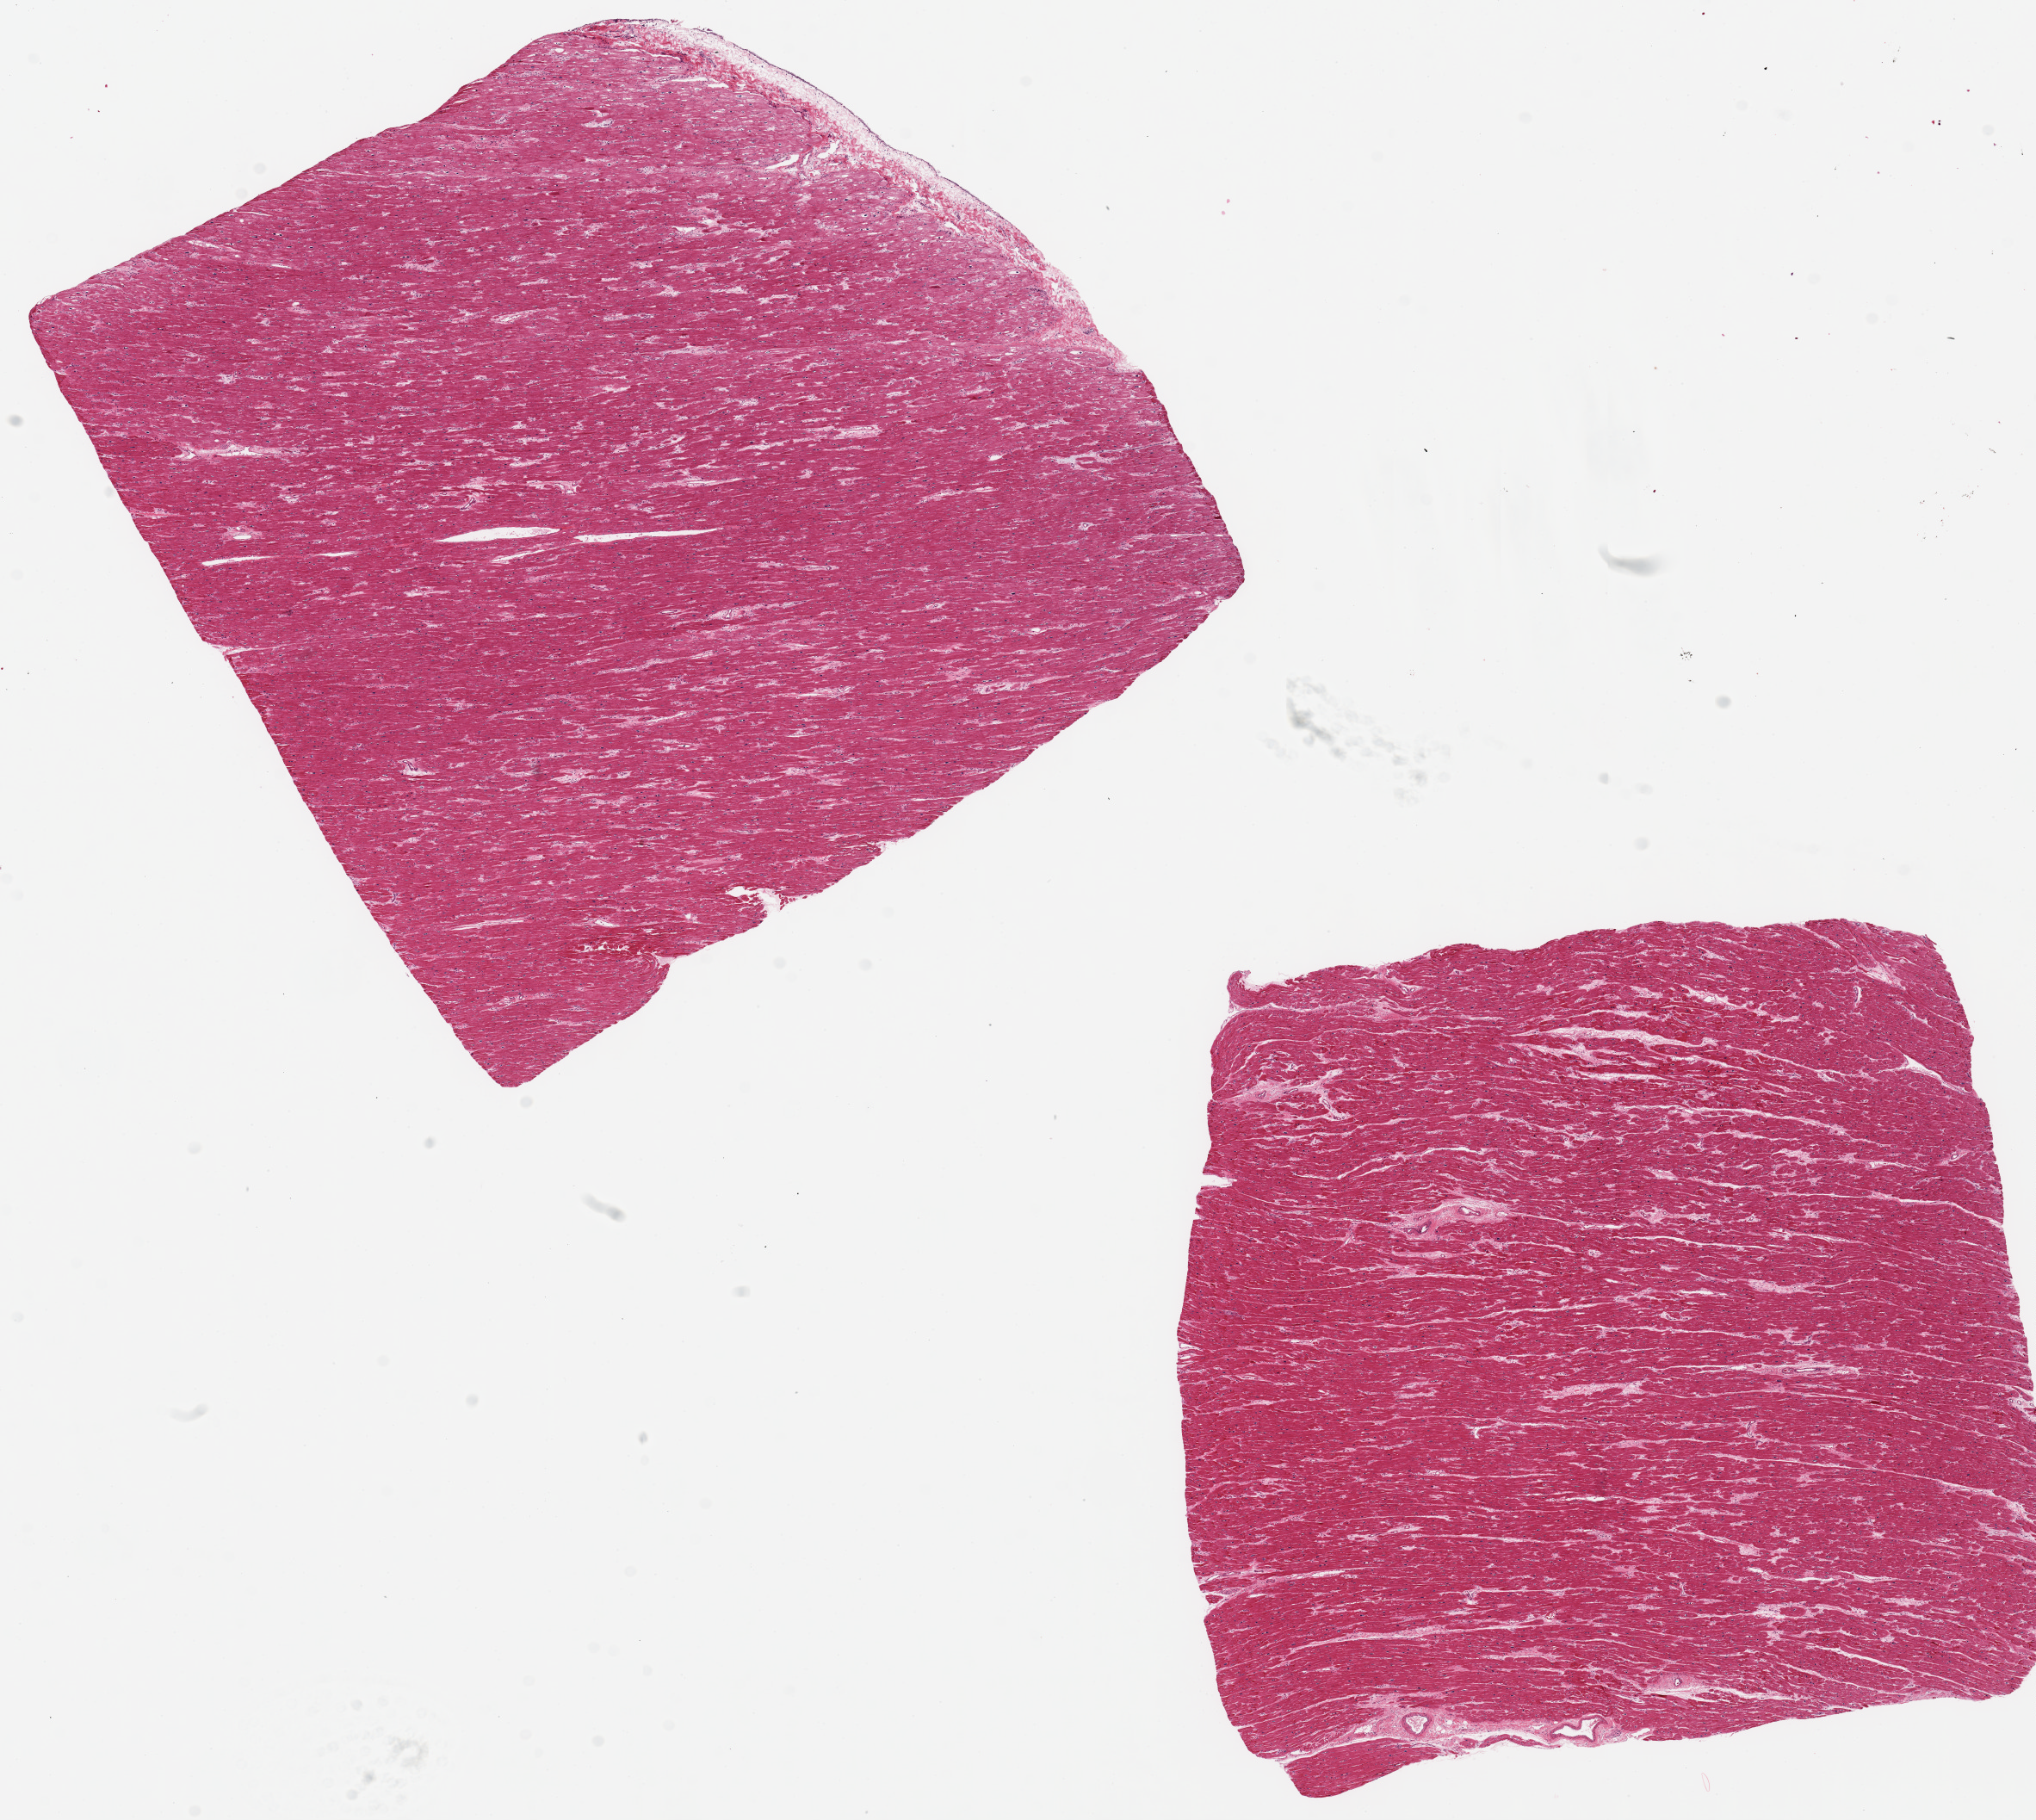
Digitized H&E-stained section, a low-resolution overview of the entire scanned area, about 18.7 x 16.7 mm, PAXgene-fixed paraffin-embedded (PFPE) section, target tissue: heart, tissue donor sample. Donor: female.
• review note (as recorded): 2 pieces, 8.5x8 & 8x8mm; minimal fibrosis